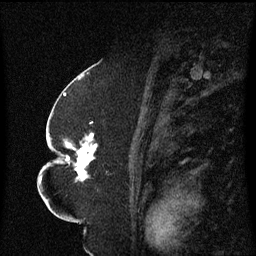
Breast MRI (dynamic contrast-enhanced), one sagittal slice; slice 36 of 60 in the series (ordered by position); dynamic contrast-enhanced series, image 2 of 3 at this slice position (ordered by acquisition); 1.5 T; TE 4.2 ms, TR 8.4 ms; 2.3 mm slice thickness; 256 × 256 image matrix, field of view 200 × 200 mm. Patient: female, 52 years. From the clinical record (not read from this slice): setting: breast cancer imaged before/during neoadjuvant chemotherapy; receptor status: HR-positive, HER2-negative.
Annotated regions visible in this slice (semi-automatically segmented with operator editing):
- analysis volume of interest (the breast-tissue region the enhancement analysis was run in; not a lesion): bounding box (x1, y1, x2, y2) in pixels: (49, 124, 108, 183)
- tumour enhancement mask (voxels above the 70 % enhancement threshold inside the analysis volume of interest): (65, 134, 97, 181)